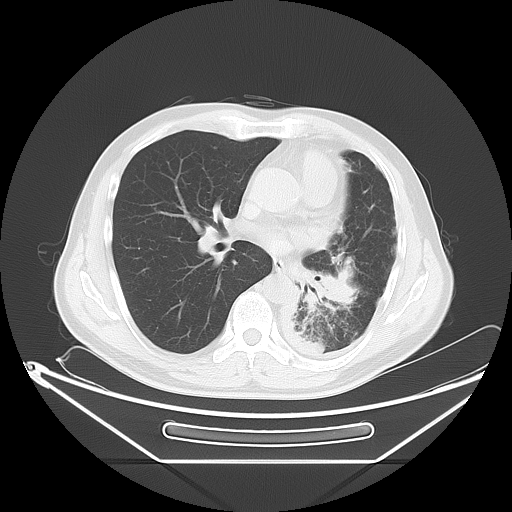
Chest CT, one axial slice. Slice 32 of 63 in the series (ordered by position). Reconstruction kernel LUNG. 120 kVp. Lung window (W 1500 / L -600 HU). 5 mm slice thickness. 512 × 512 image matrix. Patient: male, 60 years. Case-level facts recorded for this patient, not image findings: clinical TNM (as recorded): T4 N1 M1.
Structures marked on this image (bounding box drawn by a radiologist):
- lung tumour (recorded histology: adenocarcinoma): bounding box [x1, y1, x2, y2] px = [297, 250, 360, 324]